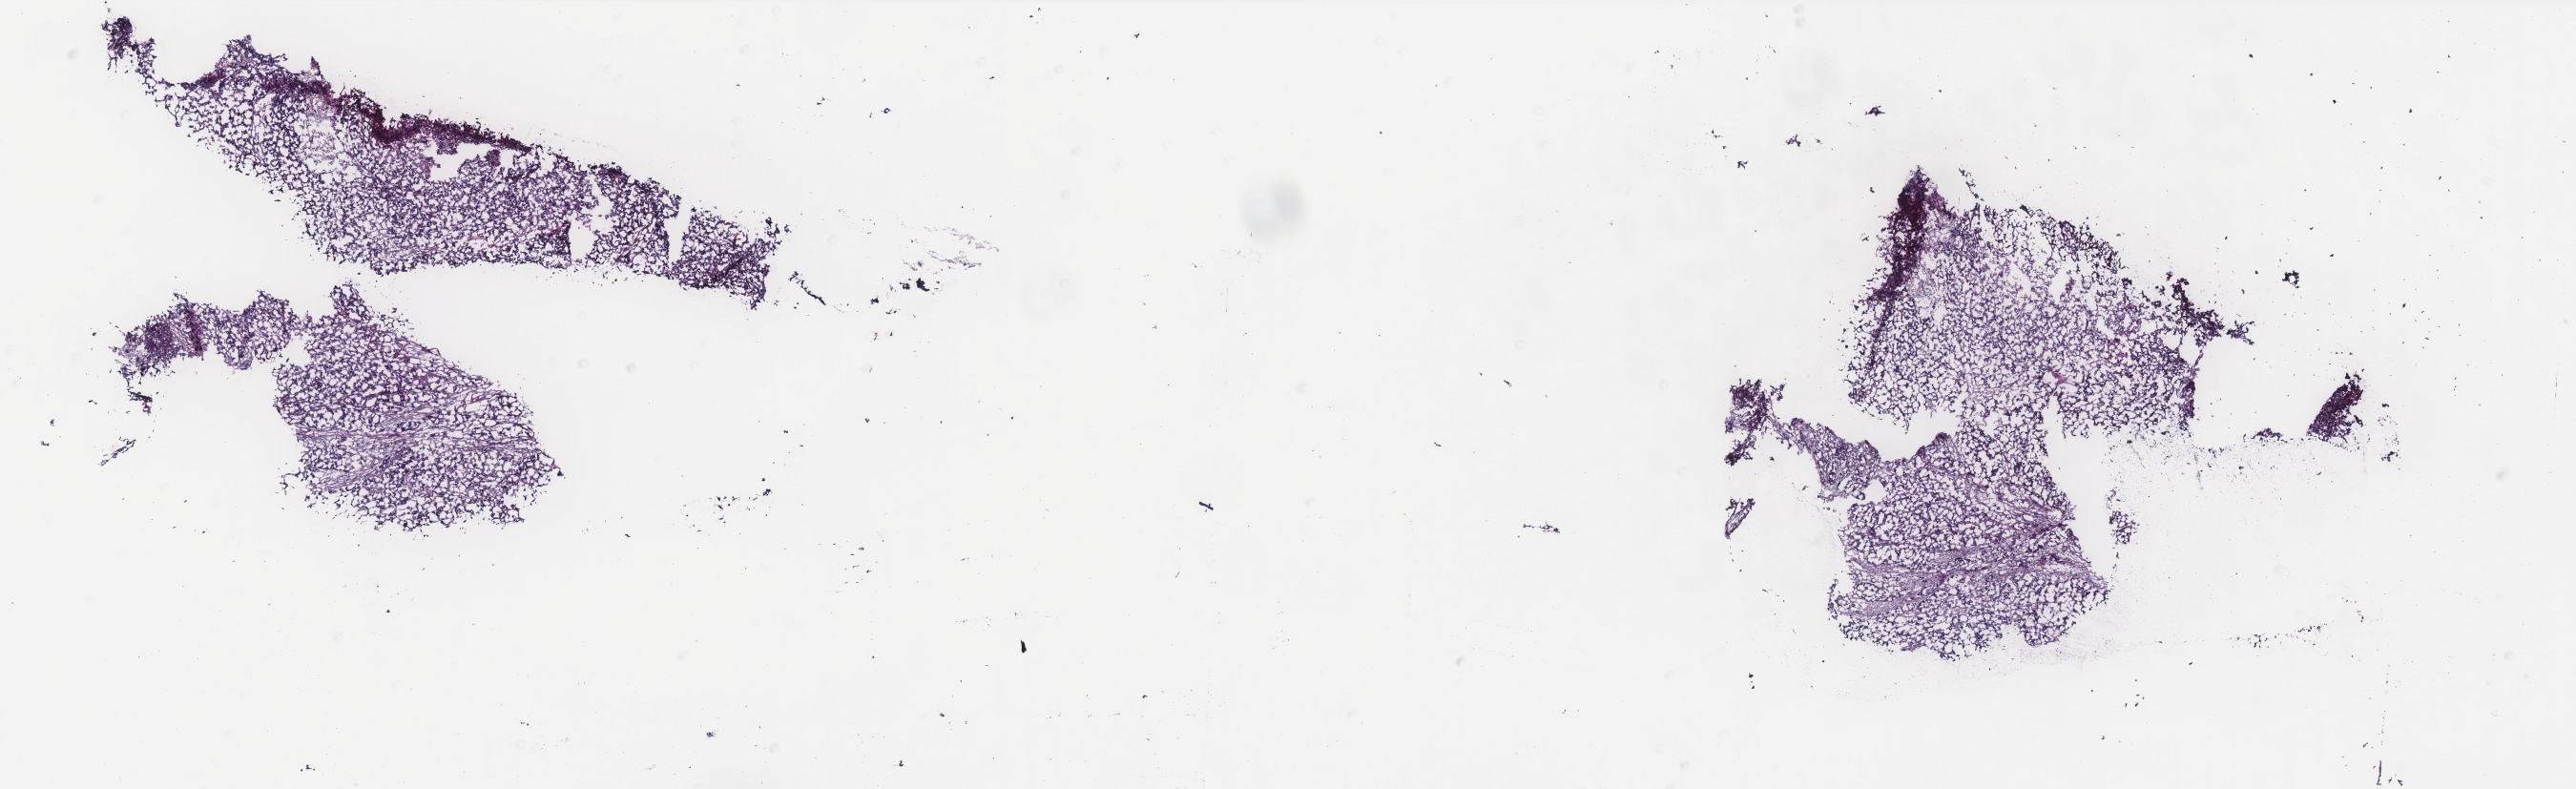
Digitized H&E-stained tissue section (whole slide) — a low-resolution overview of the entire scanned area, about 21.6 x 6.6 mm; frozen section from the top of the tissue portion; primary tumour sample from the uterus. Female, age 77 years at initial diagnosis. Histologic grade: G3 (poorly differentiated). Pathologist review of this section (percent, as recorded): tumour cells 75%, tumour nuclei 80%, normal cells 0%, stromal cells 20%, necrosis 5%. Infiltration values recorded for this section: lymphocyte infiltration 1%, monocyte infiltration 1%, neutrophil infiltration 0%.
- diagnosis: Serous cystadenocarcinoma, NOS (endometrium)
- lymph nodes positive (case pathology): 1 of 12 examined
- FIGO stage: IIIC